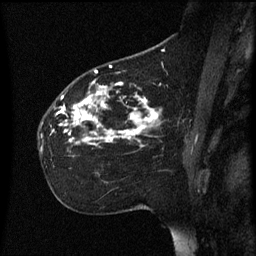
Breast MRI (dynamic contrast-enhanced), one sagittal slice; position 37 of 60 along the scan axis; dynamic contrast-enhanced series, image 2 of 3 at this slice position (ordered by acquisition); 1.5 T; TE 4.2 ms, TR 8.4 ms; 256 × 256 image matrix. Female patient, age 35 years. Case-level facts recorded for this patient, not image findings: setting: breast cancer imaged before/during neoadjuvant chemotherapy; receptor status: HER2-positive.
Annotated regions visible in this slice (semi-automatically segmented with operator editing):
- analysis volume of interest (the breast-tissue region the enhancement analysis was run in; not a lesion): bounding box <39,78,165,161> (left, top, right, bottom; pixels)
- tumour enhancement mask (voxels above the 70 % enhancement threshold inside the analysis volume of interest): <53,82,159,145>